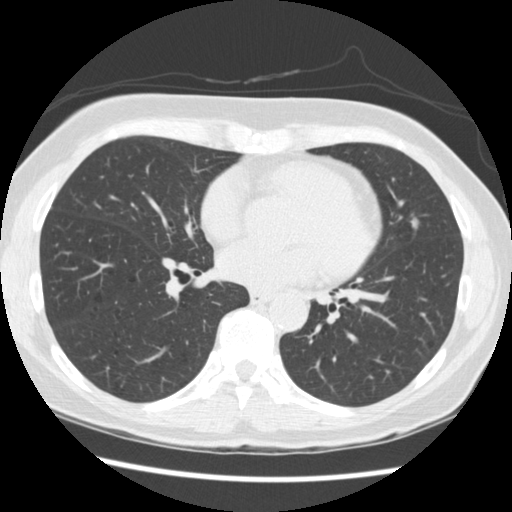
Low-dose screening chest CT, one axial slice. Lung window (W 1500 / L -600 HU). 2.5 mm slice thickness. 512 × 512 image matrix.
Structures marked on this image (manually delineated by an expert):
- lesion 2 (tumor, lingular bronchus): box from (x=410, y=218) to (x=418, y=227) px